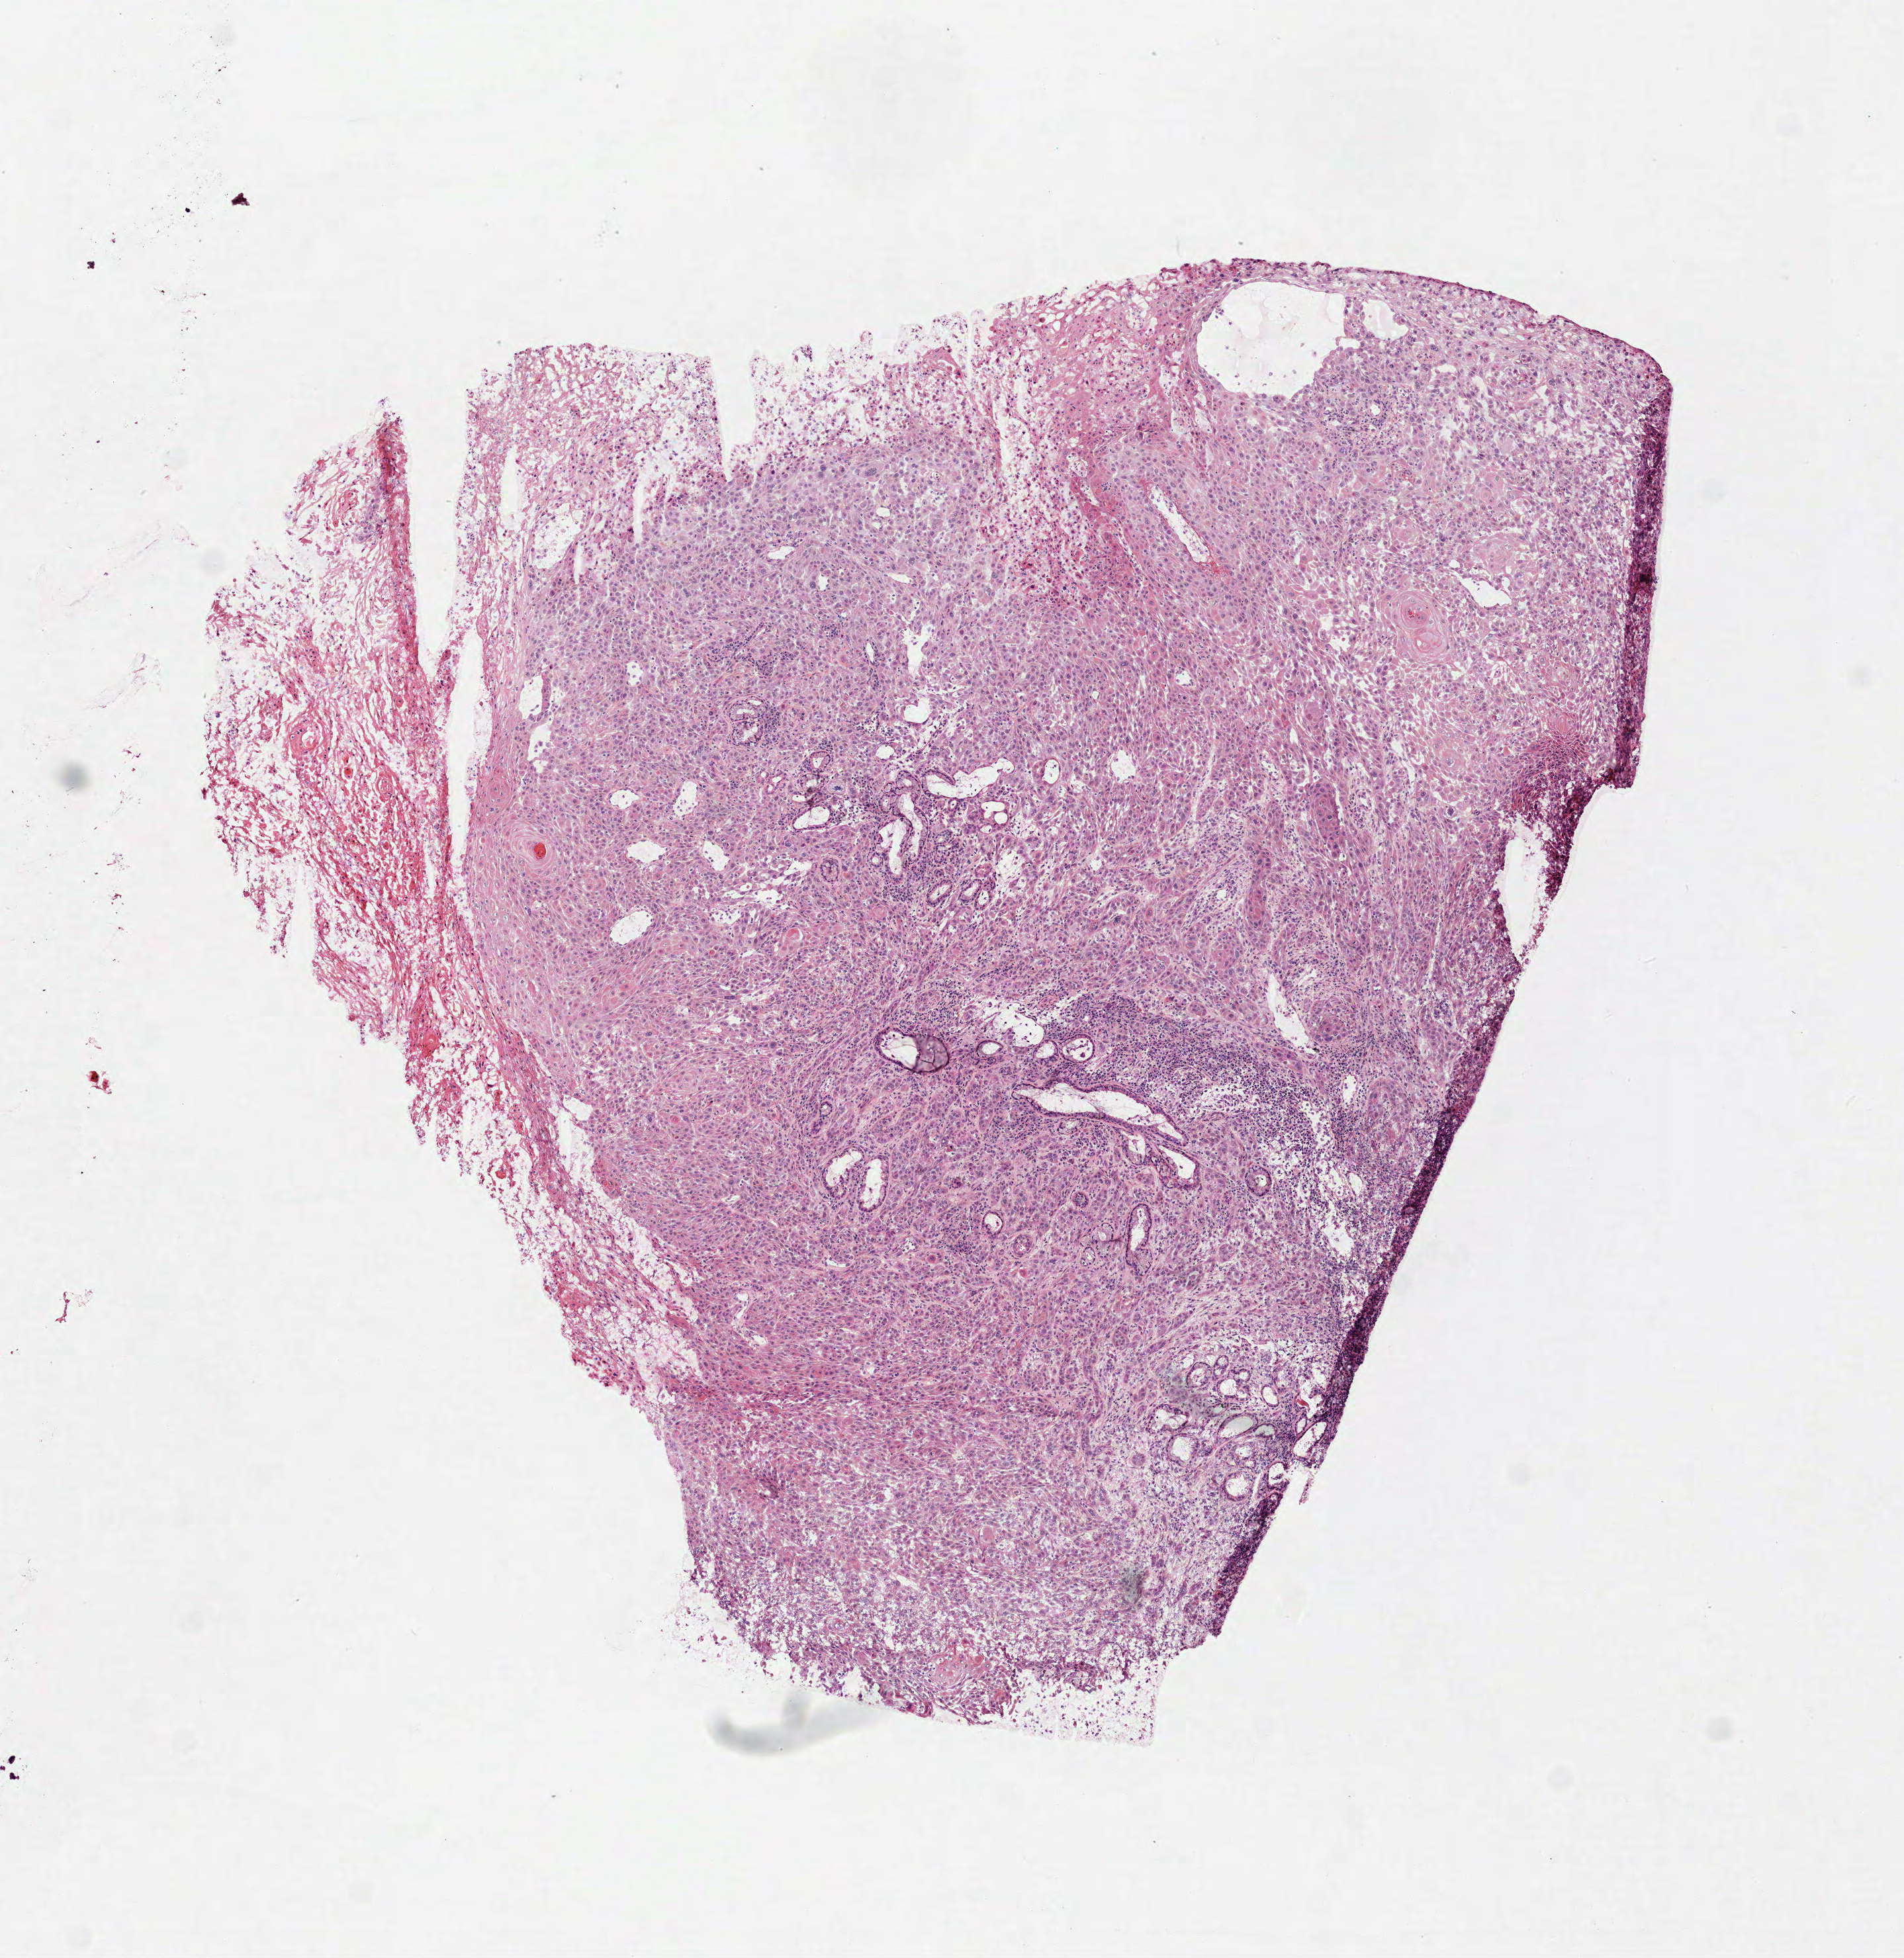
Digitized H&E-stained tissue section (whole slide), whole scanned area (about 5.8 x 6.0 mm, acquisition: 40x scan) shown as a low-resolution overview; frozen section from the top of the tissue portion; primary tumour sample from the head and neck. Male patient; age at initial diagnosis 59 years. Histologic grade: G2 (moderately differentiated). Pathologist review of this section (percent, as recorded): tumour cells 80%, tumour nuclei 80%, normal cells 0%, stromal cells 10%, necrosis 10%.
TNM: T3 N0. Histologic diagnosis: Squamous cell carcinoma, NOS (larynx, NOS). AJCC pathologic stage: III (7th edition).